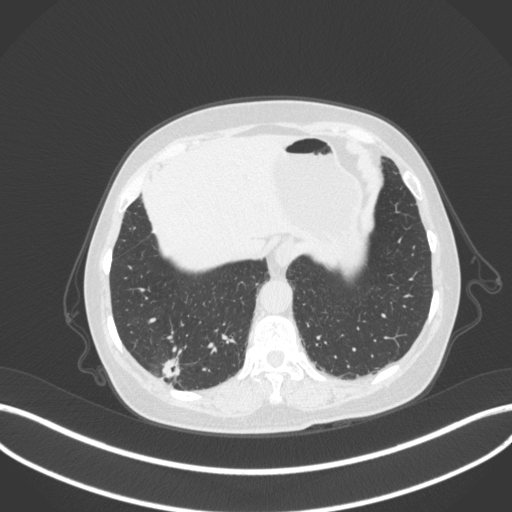
Chest CT, one axial slice. Position 54 of 340 along the scan axis. Reconstruction kernel B31f. 120 kVp. Lung window (W 1500 / L -600 HU). 512 × 512 image matrix. Female patient, age 69 years. From the clinical record (not read from this slice): clinical TNM (as recorded): T1b N0 M0; histopathological grade: G2-3.
Structures marked on this image (bounding box drawn by a radiologist):
- lung tumour (recorded histology: adenocarcinoma): bounding box (x1, y1, x2, y2) in pixels: (155, 352, 187, 385)